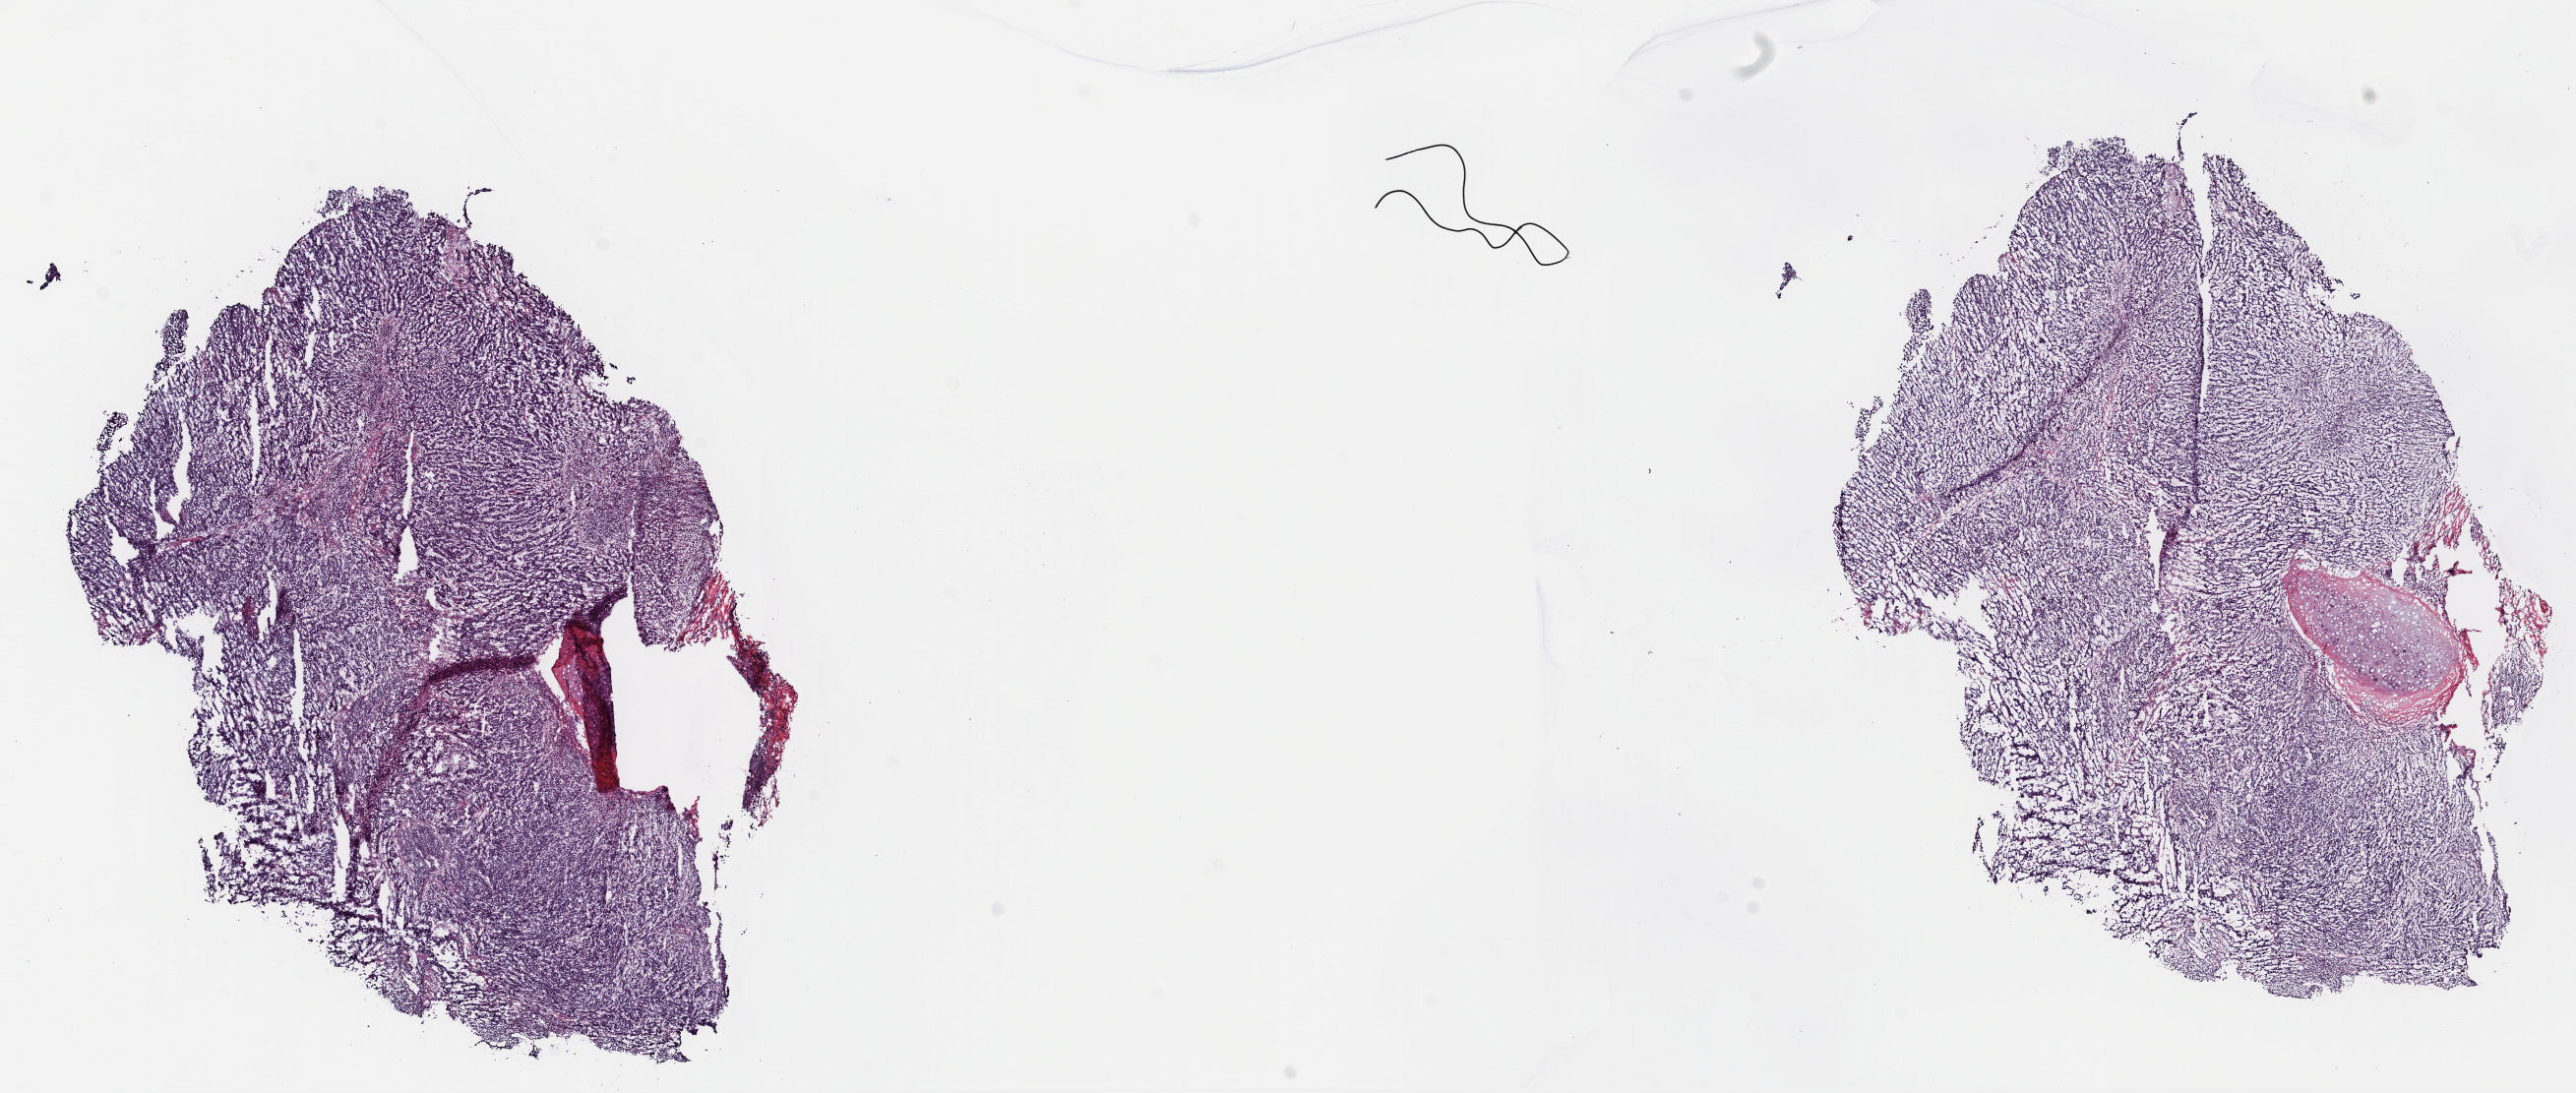
H&E whole-slide image — low-resolution overview of the scanned area, about 20.6 x 8.7 mm (slide scanned at 40x), frozen section, lung, primary tumour sample. Female patient; age at initial diagnosis 57 years.
Histologic diagnosis: Squamous cell carcinoma, NOS (lower lobe, lung).